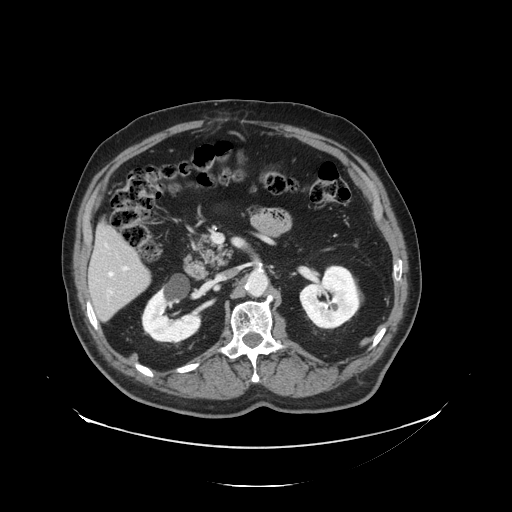
Contrast-enhanced abdominal CT, one axial slice. Position 62 of 138 along the scan axis. Reconstruction kernel STANDARD. 120 kVp. Soft-tissue window (W 400 / L 40 HU). 2.5 mm slice thickness. 512 × 512 image matrix, field of view 497 × 497 mm. Male patient, age 77 years. From the clinical record (not read from this slice): diagnosis: colorectal cancer liver metastases, imaged before liver resection.
Structures marked on this image (manually delineated by an expert):
- liver: bounding box <91,225,150,321> (left, top, right, bottom; pixels)
- planned liver remnant (the part of the liver to remain after resection): <91,225,143,285>
- portal vein (with intrahepatic branches): <124,267,128,270>